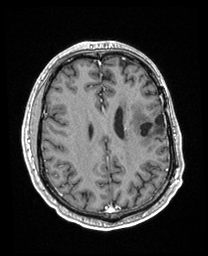
Brain MRI from a brain-tumour surgery series, one axial slice; position 83 of 208 along the scan axis; T1-weighted post-contrast; 208 × 256 image matrix, field of view 211 × 260 mm. From the clinical record (not read from this slice): histopathology: Astrocytoma; WHO grade: 3; IDH mutation: yes.
Outlined on this slice (expert manual segmentation):
- previous resection cavity: bounding box (x1, y1, x2, y2) in pixels: (141, 114, 165, 136)